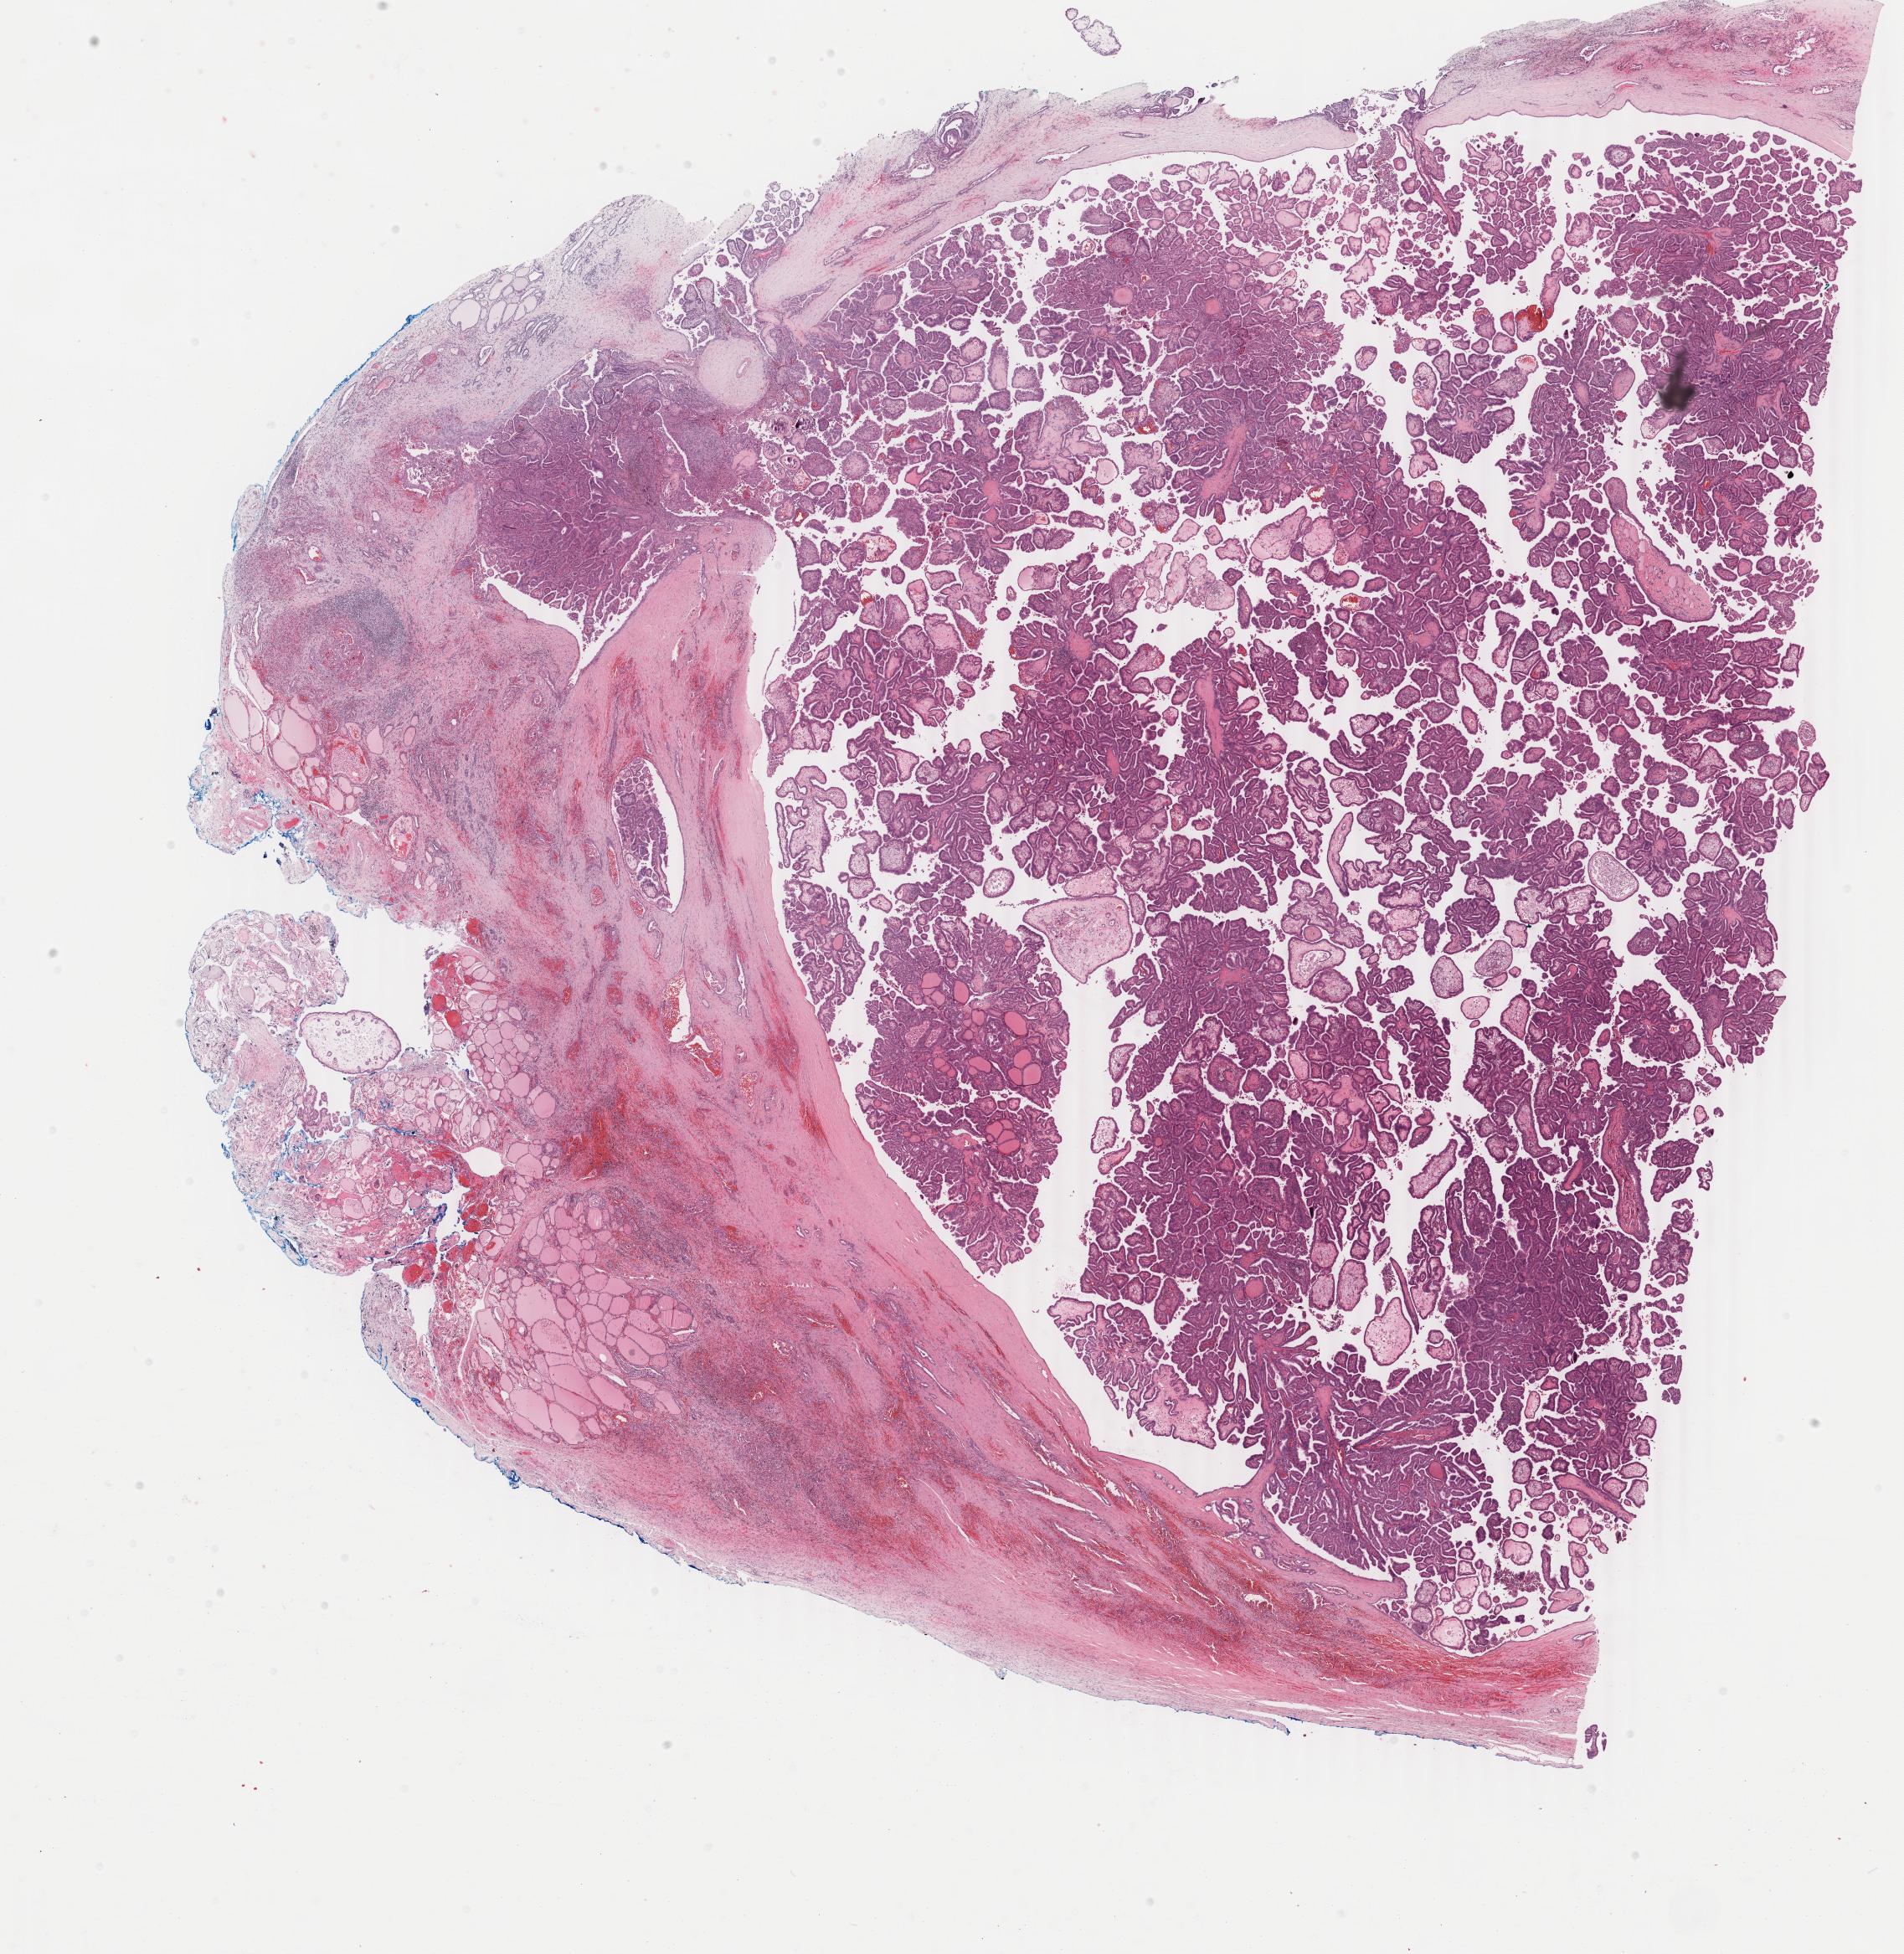
H&E-stained whole-slide image, a low-resolution overview of the entire scanned area, about 18.1 x 18.6 mm (slide scanned at 40x). Formalin-fixed paraffin-embedded (FFPE) diagnostic section. Thyroid, primary tumour sample. Patient: female, age at initial diagnosis 26 years.
* laterality: right
* histologic diagnosis: Papillary adenocarcinoma, NOS (thyroid gland)
* lymph nodes positive (case pathology): 2 of 2 examined
* AJCC pathologic stage: I (6th edition)